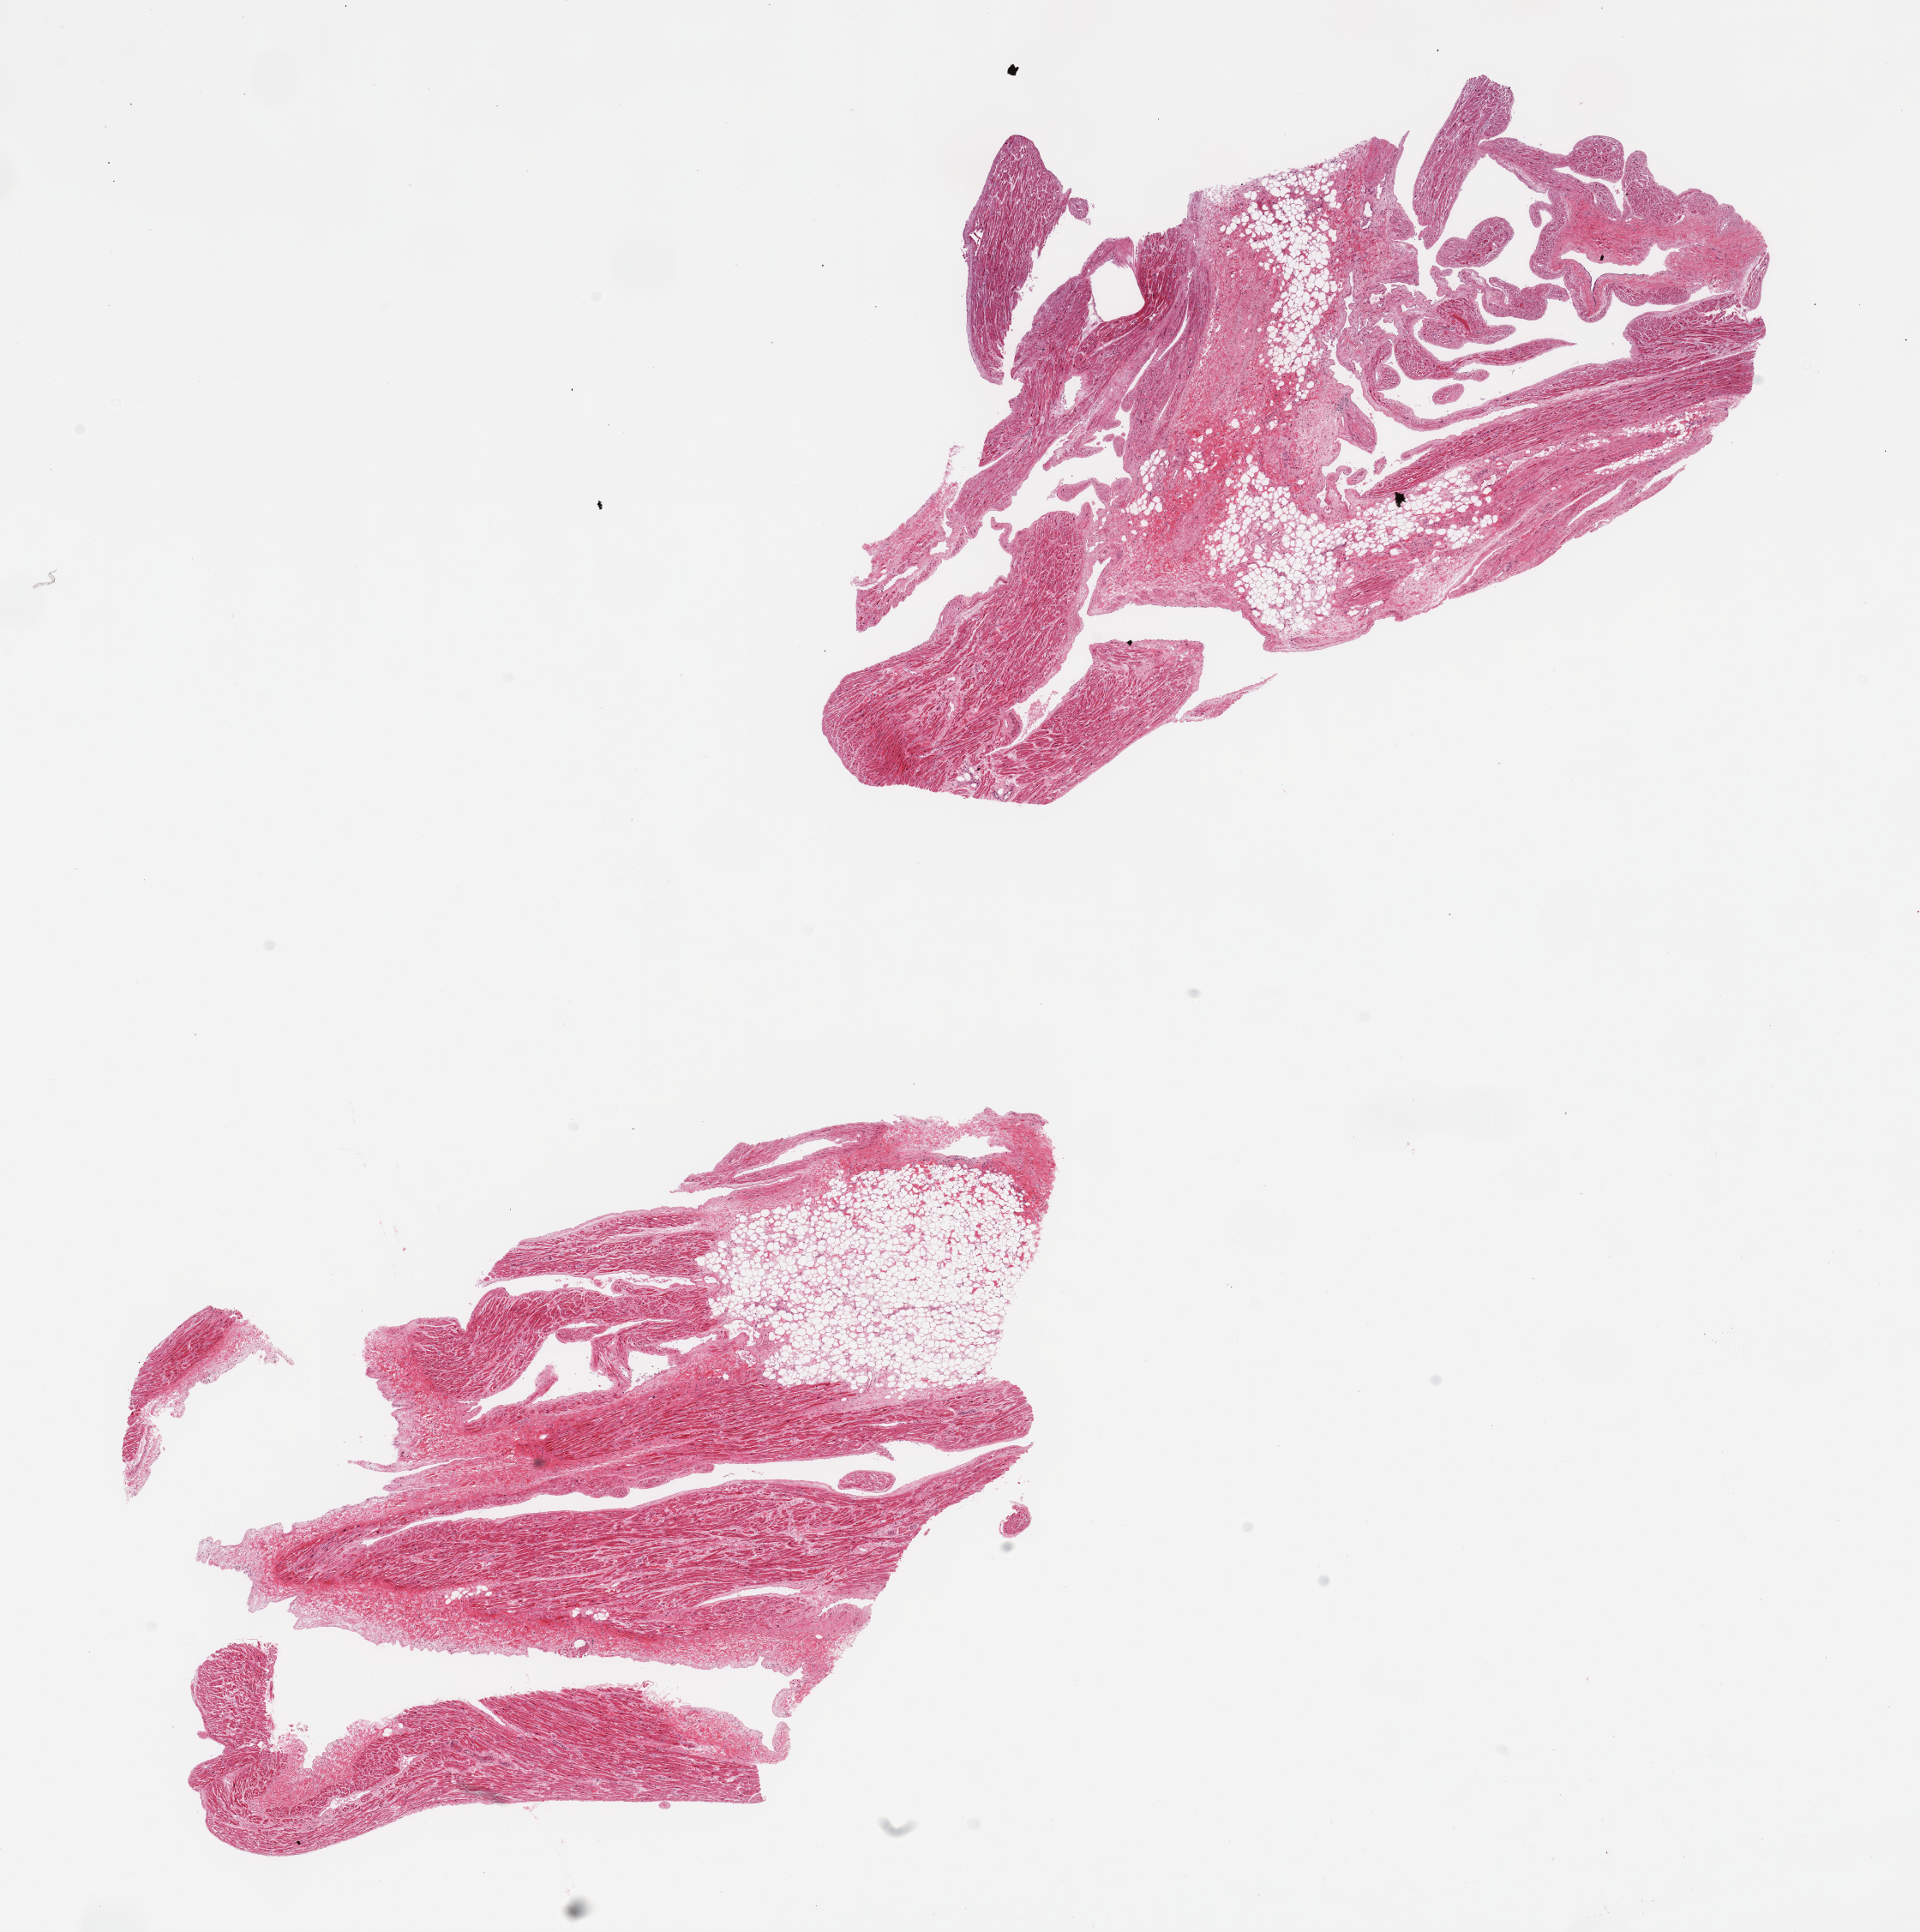
Digitized hematoxylin and eosin (H&E)-stained section — whole scanned area (about 17.7 x 17.8 mm) shown as a low-resolution overview, PAXgene-fixed paraffin-embedded (PFPE) section, target tissue: auricular appendage, donor tissue sample. Donor: male.
Pathologist's review note for this sample: 2 pieces; fibromuscular tissue with ~20% internal fat.